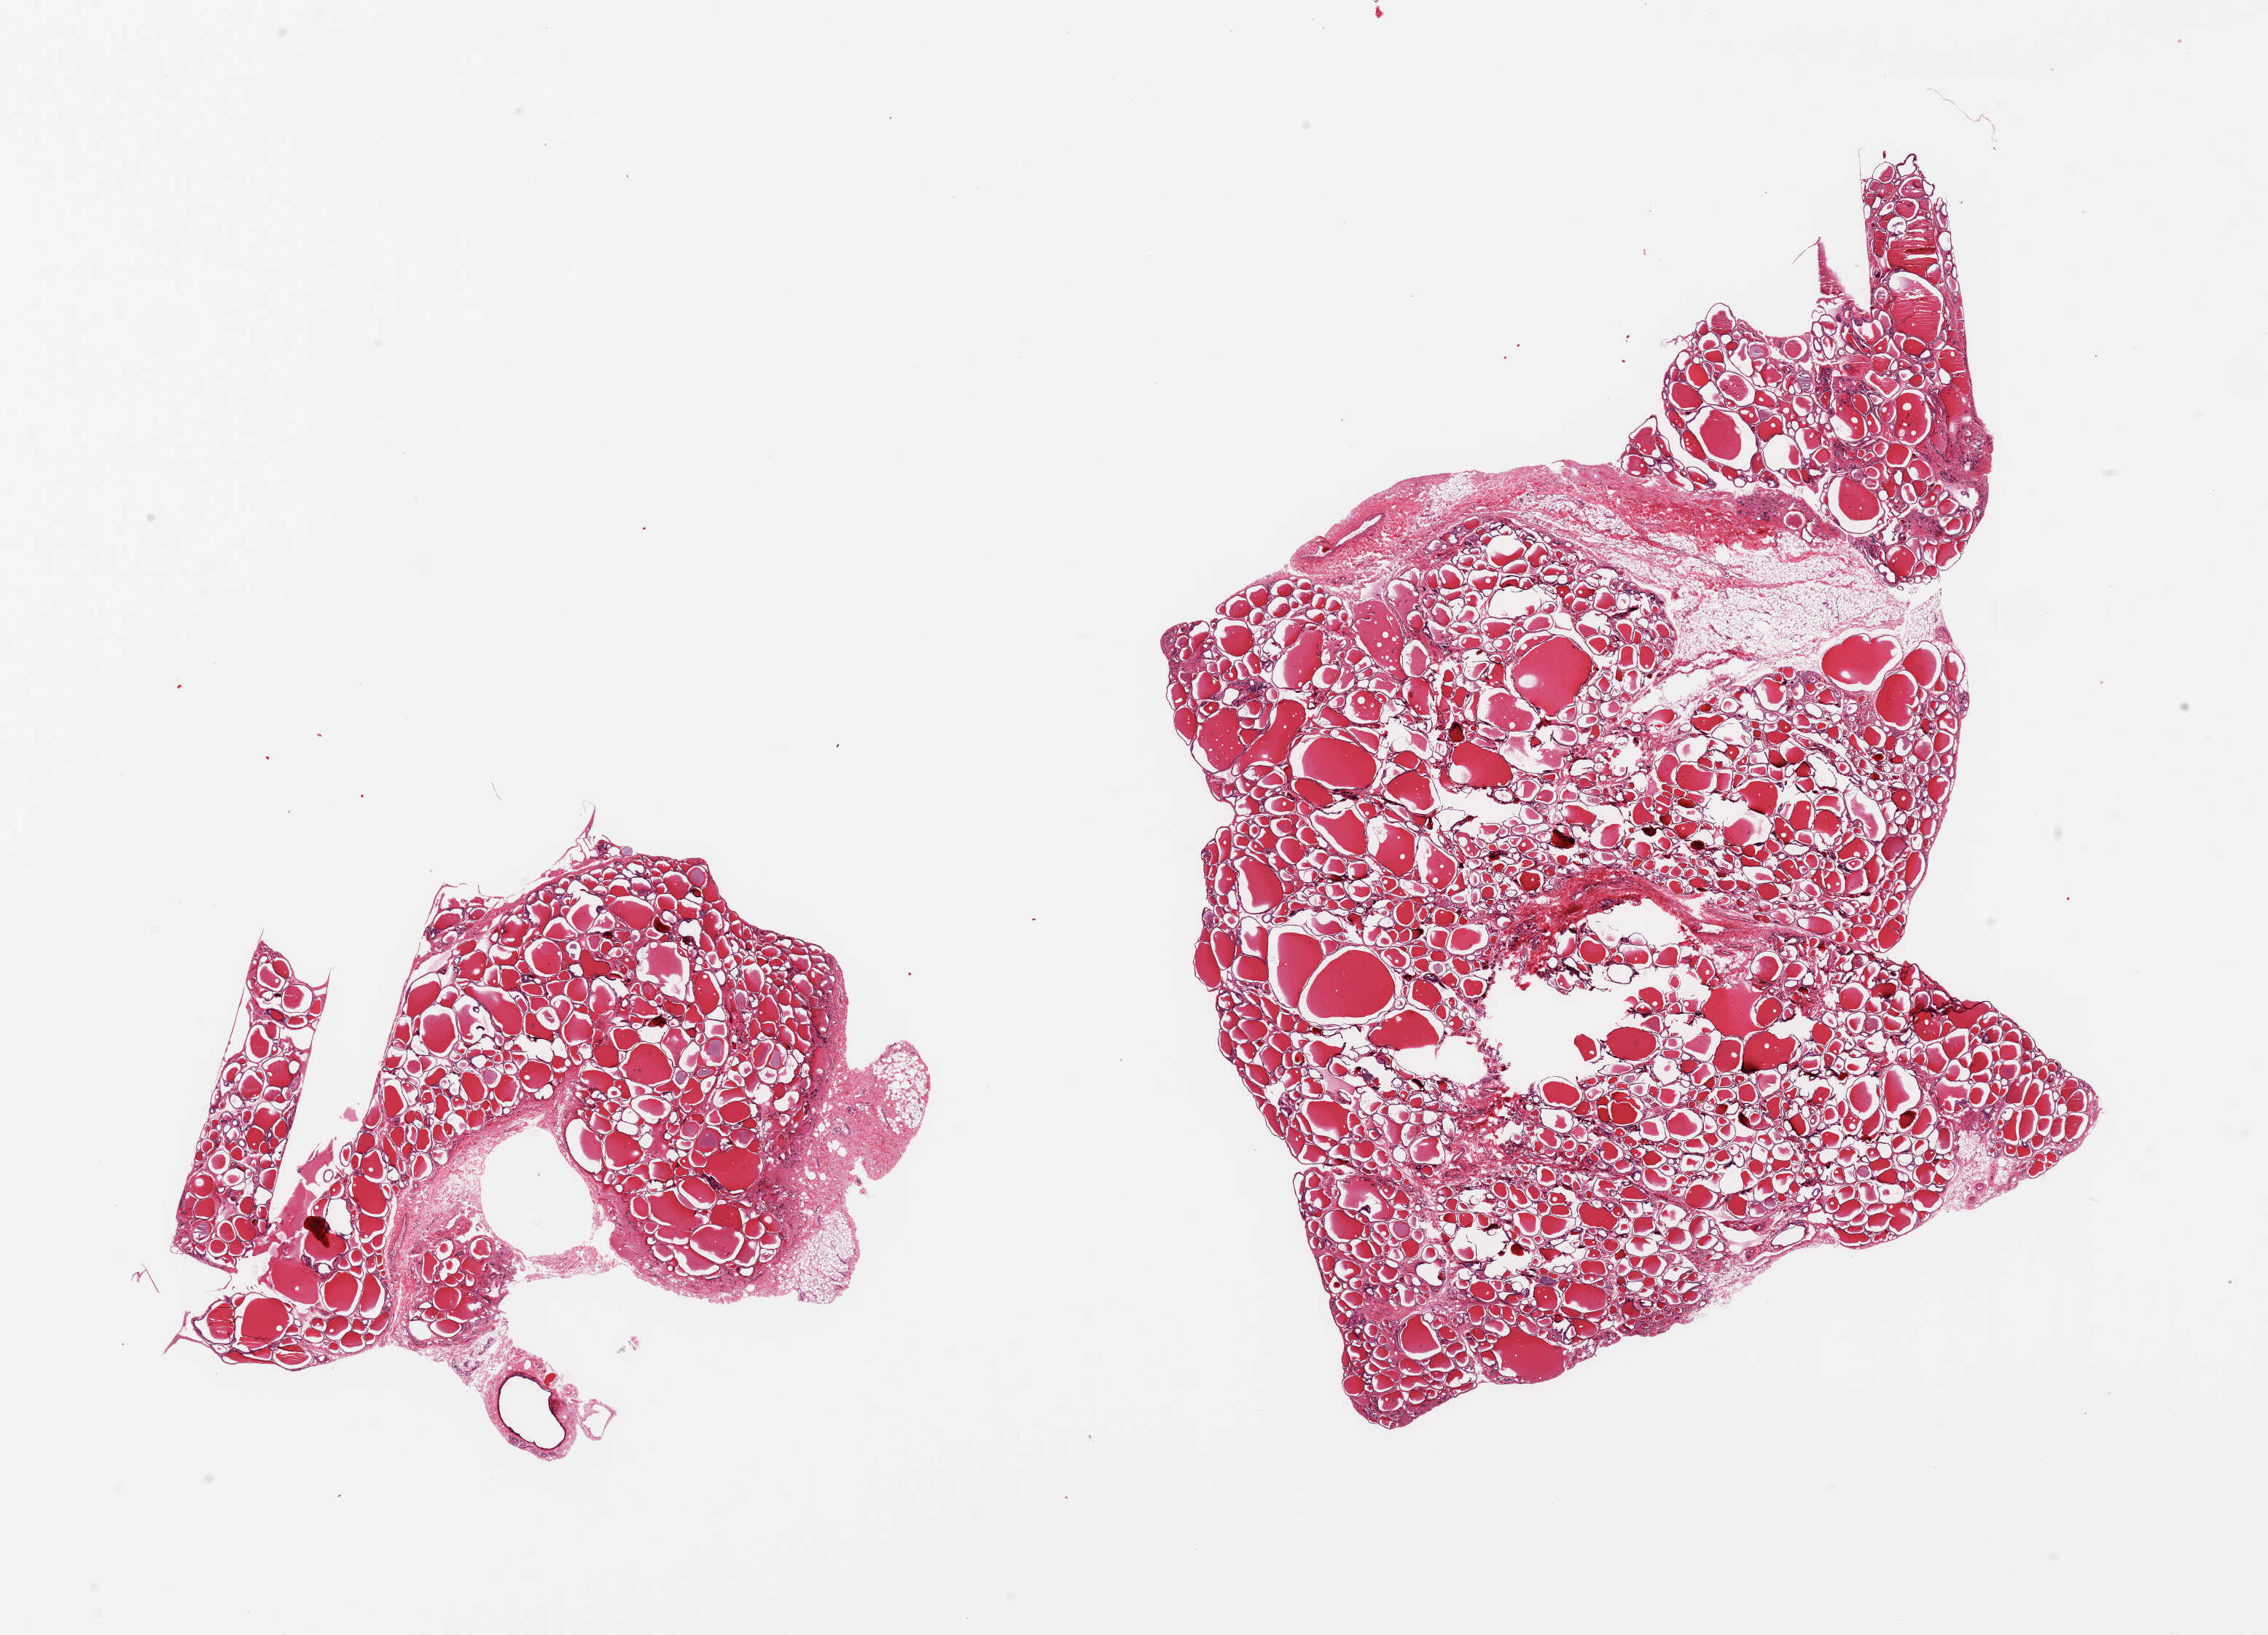
Digitized haematoxylin and eosin-stained section, shown as a low-resolution overview of the whole scanned area (about 24.6 x 17.7 mm, from a 20x scan), PAXgene-fixed paraffin-embedded (PFPE) section, section of thyroid (target tissue), donor tissue sample.
Pathologist's review note for this sample: 2 pieces, no abnormalities.